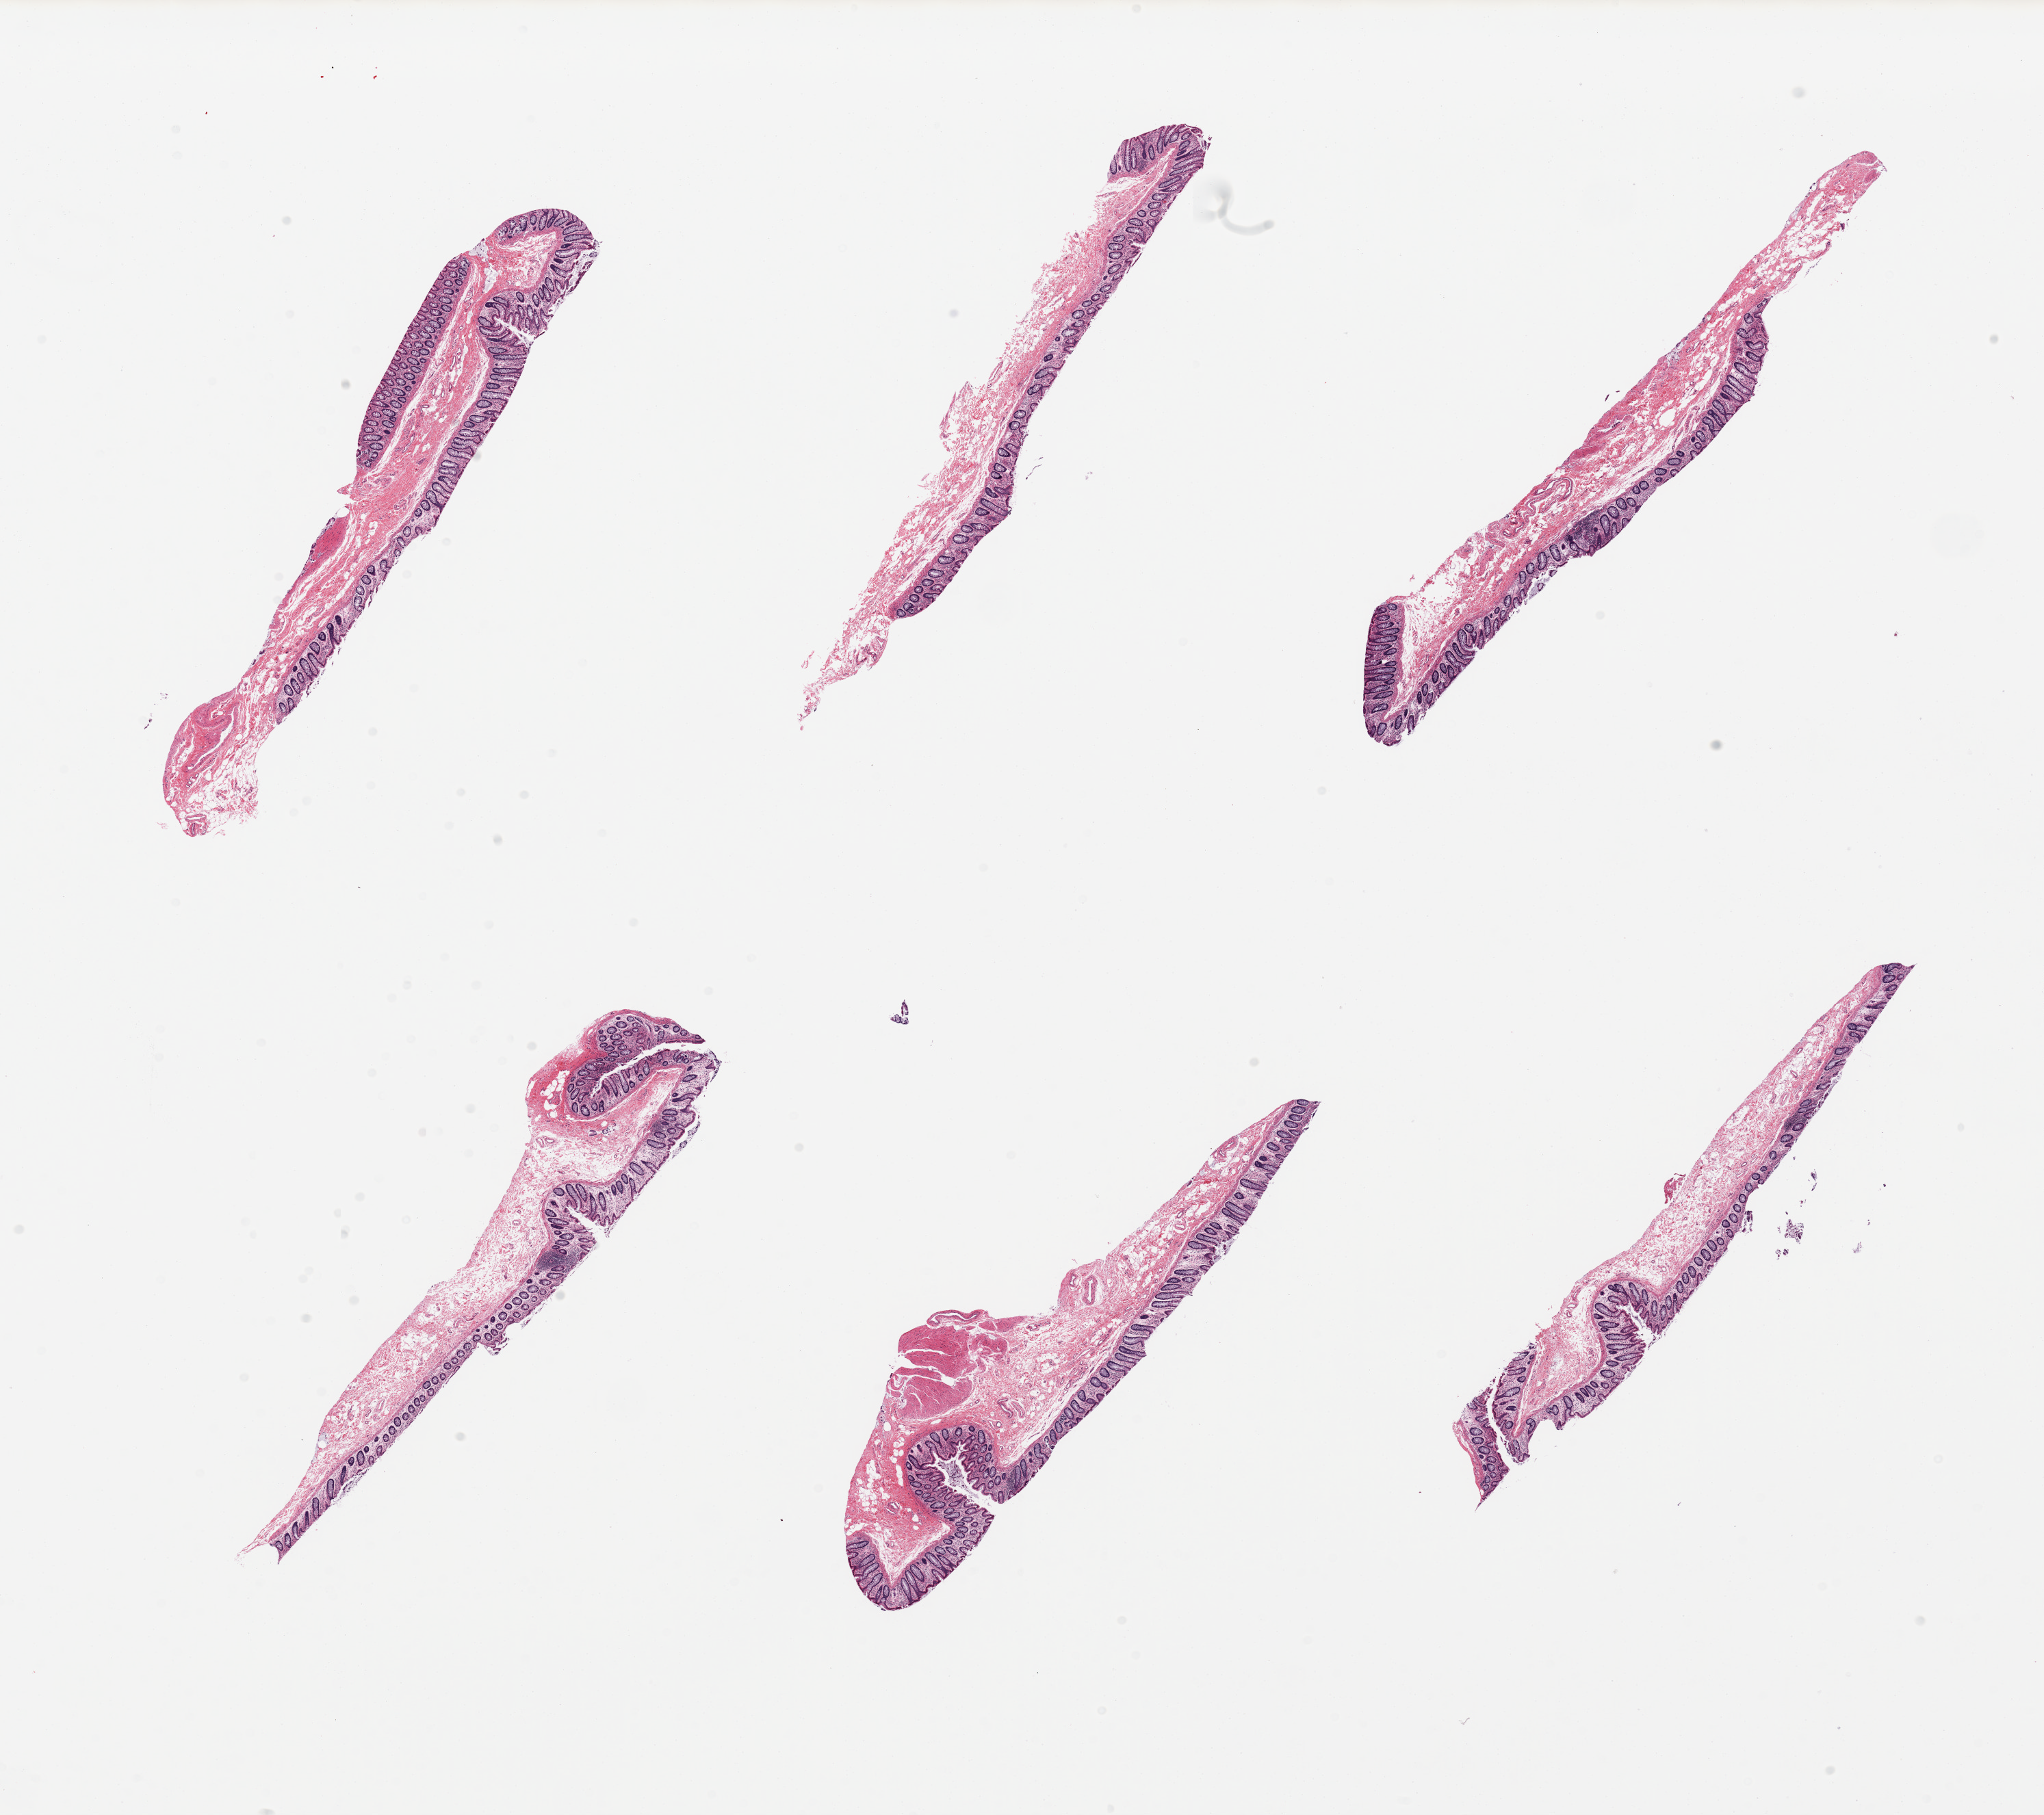
Digitized haematoxylin and eosin-stained section, shown as a low-resolution overview of the whole scanned area (about 23.6 x 21.0 mm). Donor sex: female.
Specimen: PAXgene-fixed, paraffin-embedded tissue; target tissue: ileum; donor tissue sample.